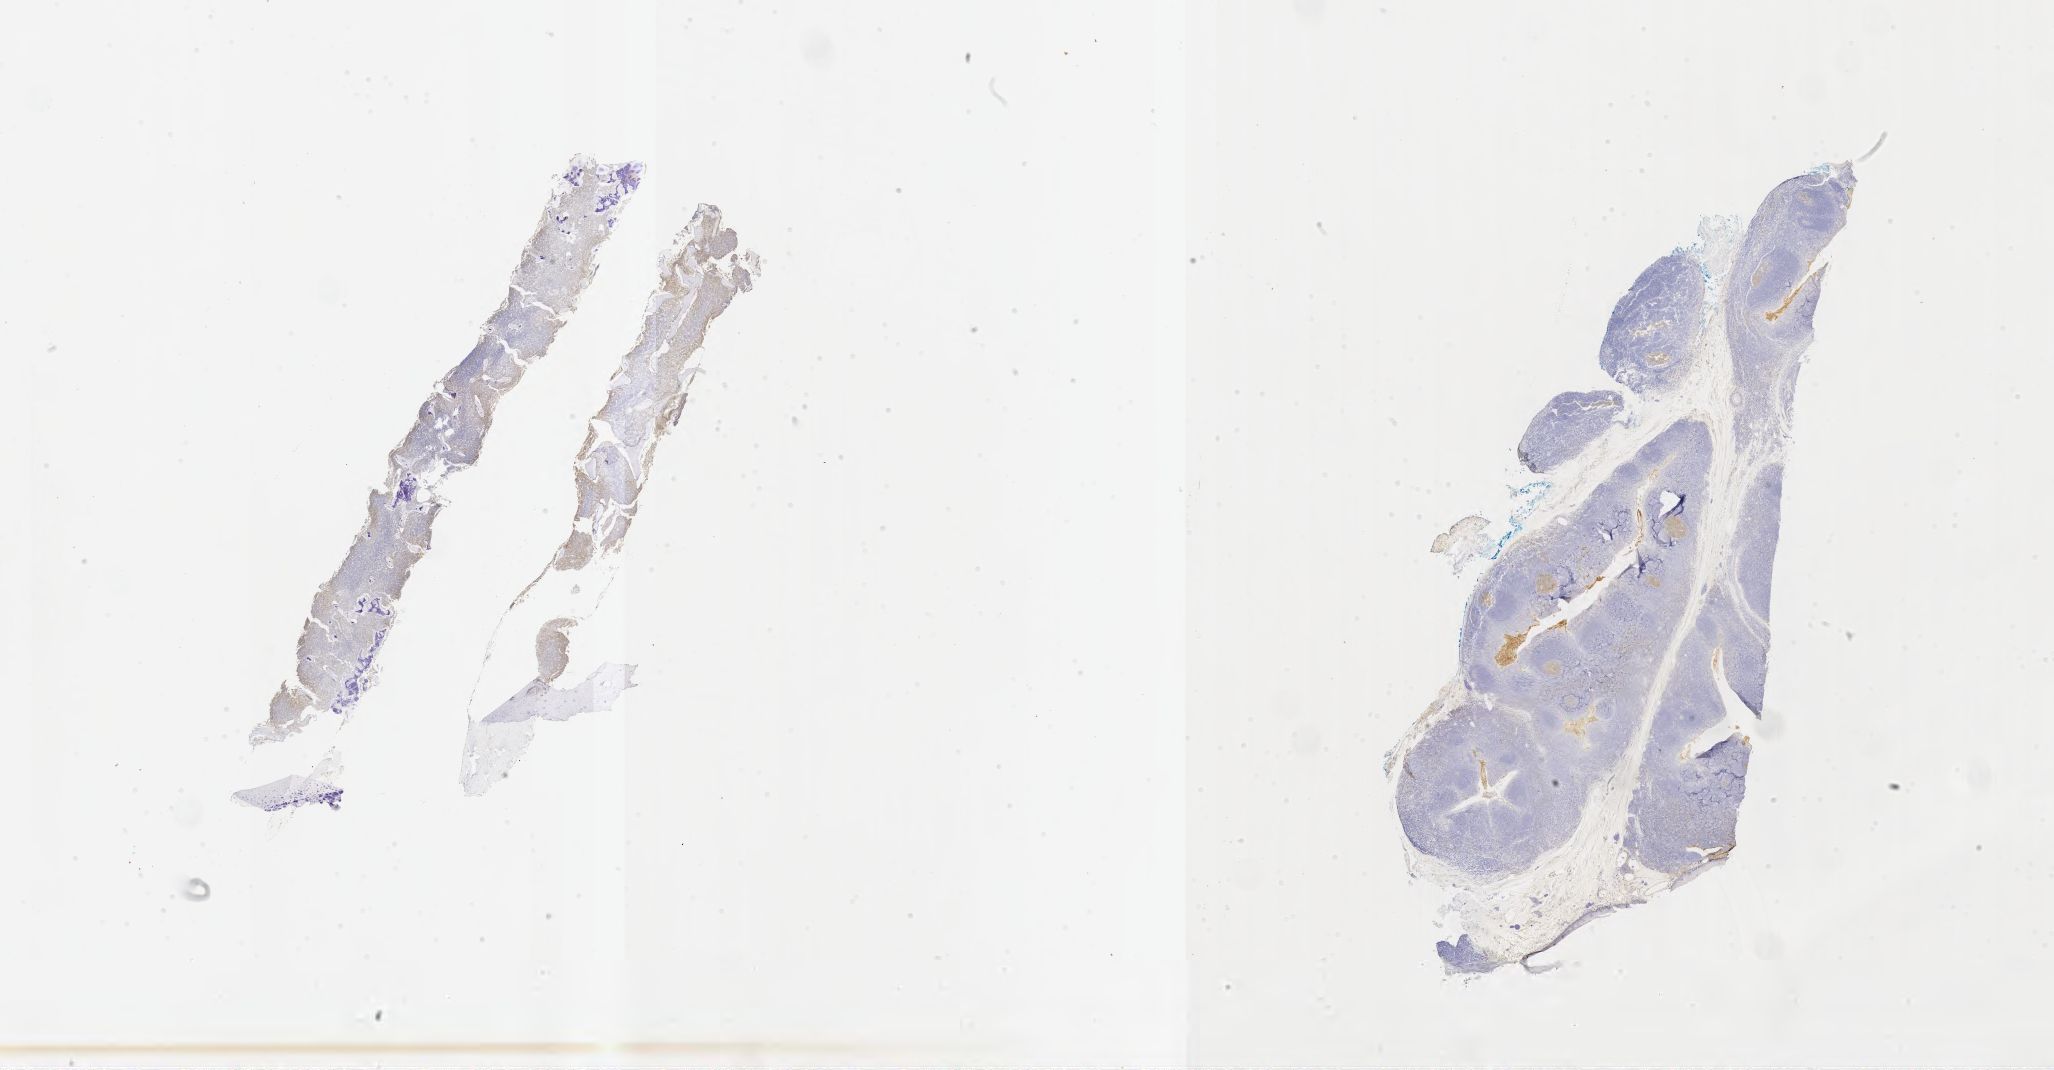
Immunohistochemistry (IHC) whole-slide image stained for CD10 — low-resolution overview of the scanned area, about 33.2 x 17.3 mm, specimen: tumor tissue, site: bone marrow. Patient male; age 16 years.
Diagnosis: Burkitt lymphoma, NOS.